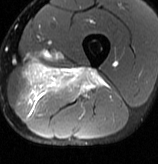
MRI of an extremity soft-tissue mass, one axial slice. Slice 28 of 70 in the series (ordered by position). T2-weighted fat-saturated. MR volume resampled by the dataset authors to the PET/CT grid (not the native acquisition matrix). 3.27 mm slice thickness. 158 × 164 image matrix, field of view 154 × 160 mm. Male patient. Case-level facts recorded for this patient, not image findings: histological type: extraskeletal osteosarcoma; grade: high; site of the primary tumour: left adductur.
Outlined on this slice (expert contour drawn on MRI and transferred to this co-registered scan by the dataset authors):
- gross tumour volume (mass): bounding box (x1, y1, x2, y2) in pixels: (22, 59, 110, 118)